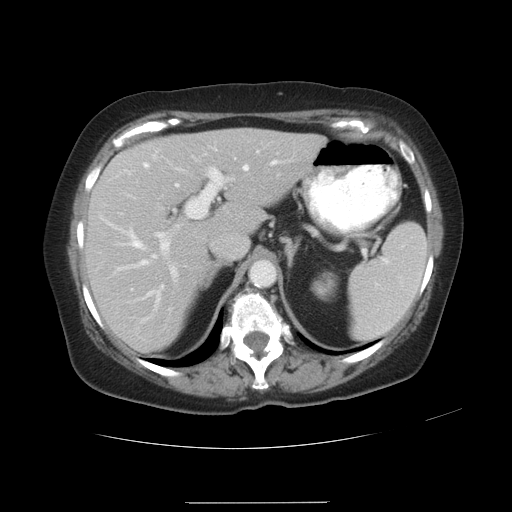
Contrast-enhanced abdominal CT, one axial slice; slice 20 of 32 in the series (ordered by position); reconstruction kernel STANDARD; 120 kVp; intravenous contrast given; soft-tissue window (W 400 / L 40 HU); 7.5 mm slice thickness; 512 × 512 image matrix, field of view 386 × 386 mm. Female patient, age 65 years. Case-level facts recorded for this patient, not image findings: diagnosis: colorectal cancer liver metastases, imaged before liver resection; multiple liver metastases: yes; largest metastasis: 1.7 cm; chemotherapy before resection: no.
Annotated regions visible in this slice (outlined manually by an expert reader):
- liver: bounding box [x1, y1, x2, y2] px = [88, 130, 321, 350]
- planned liver remnant (the part of the liver to remain after resection): [88, 135, 234, 350]
- portal vein (with intrahepatic branches): [99, 157, 250, 311]